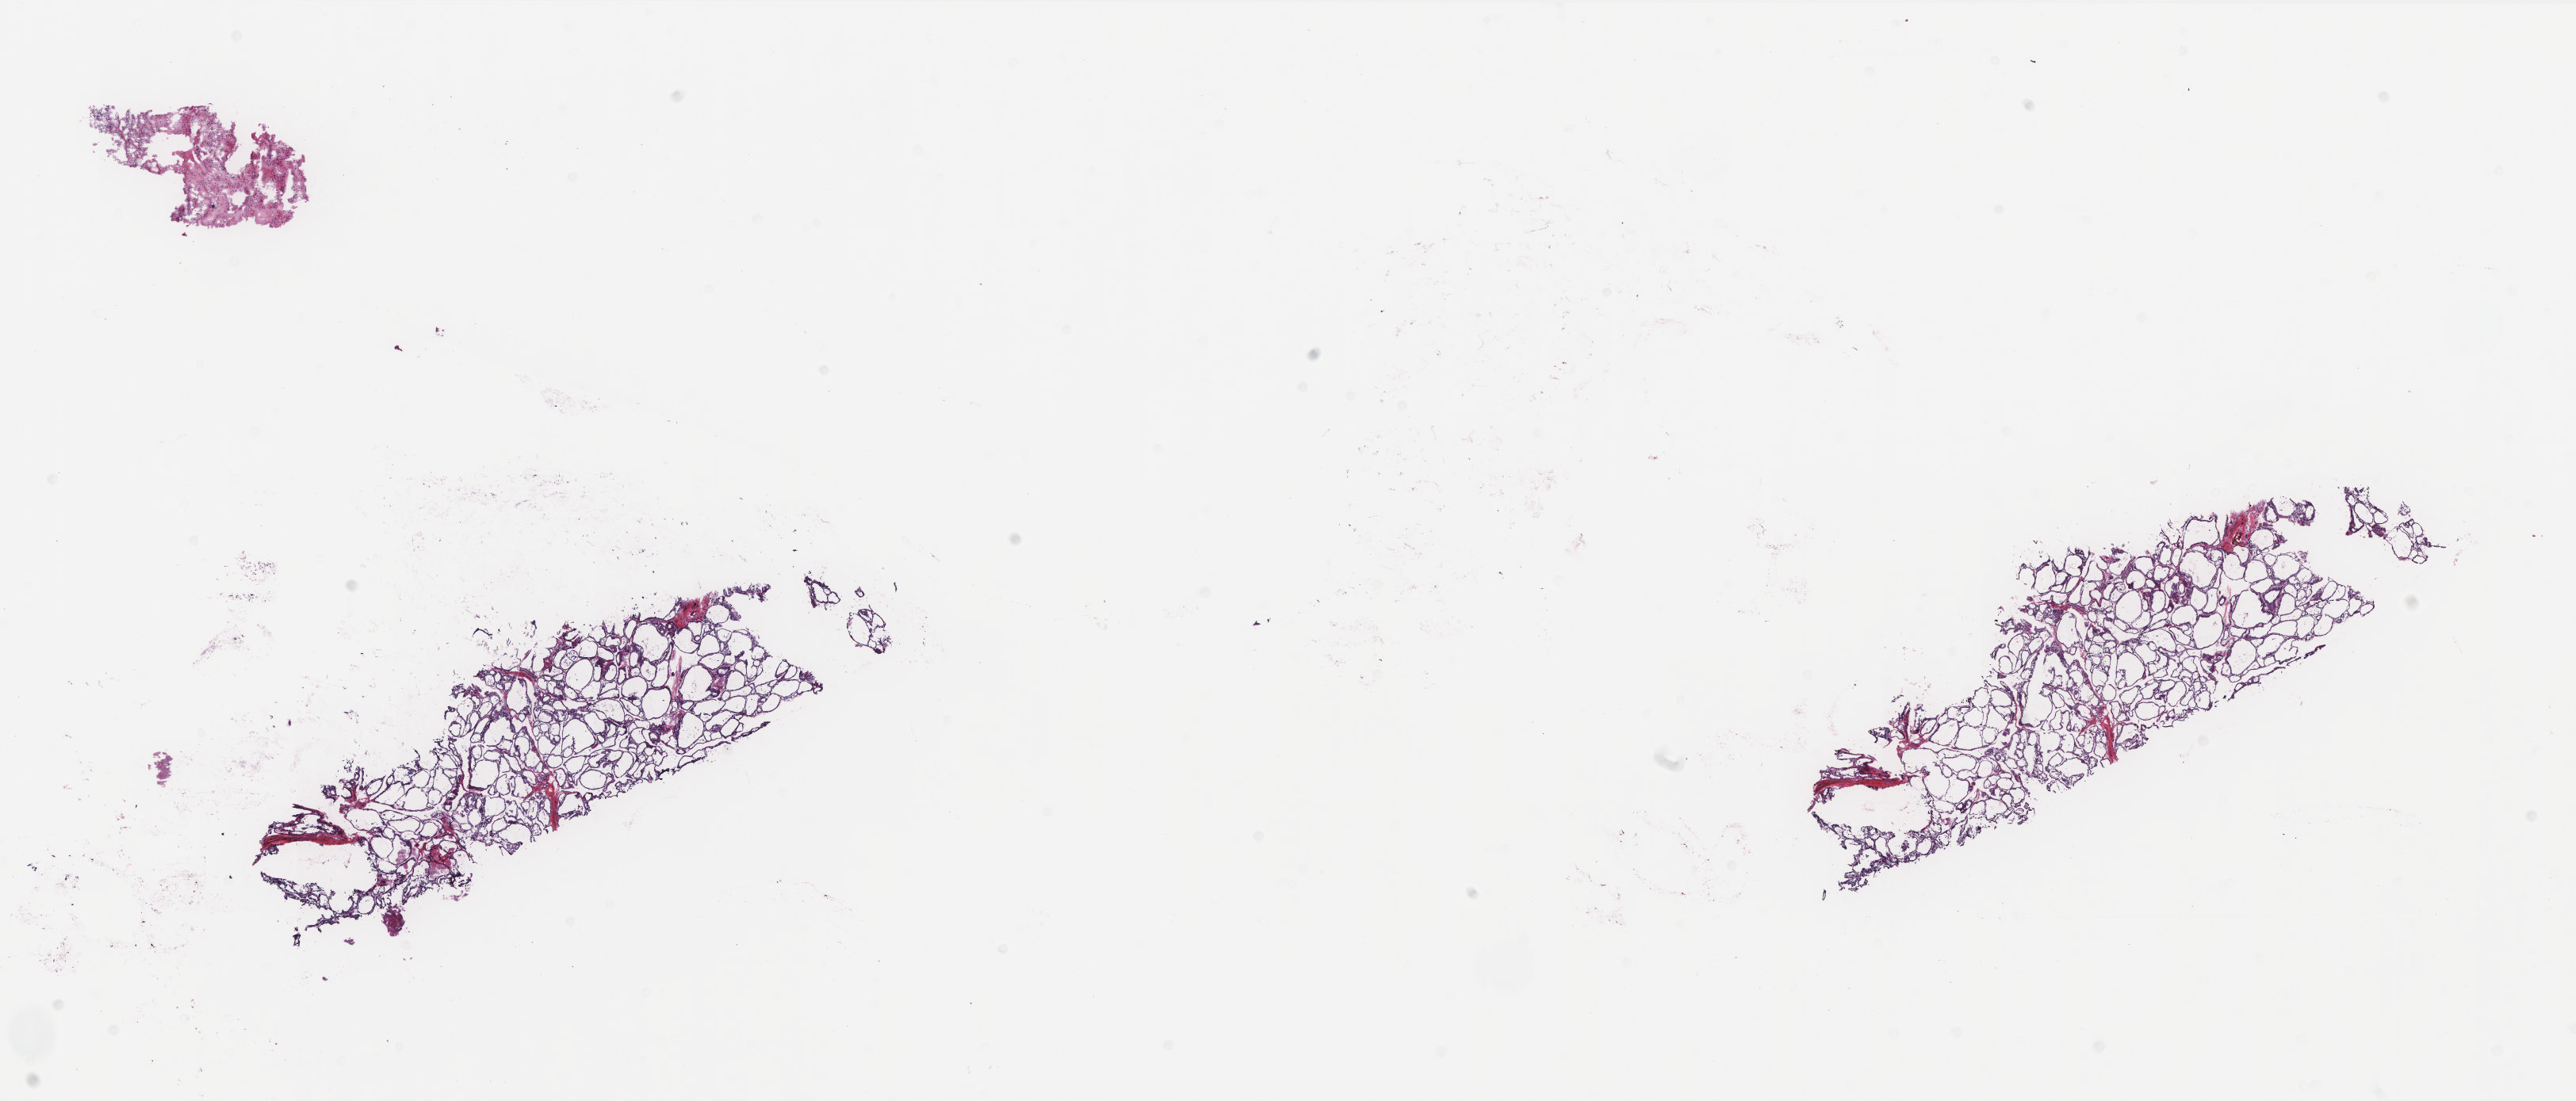
Whole-slide histology image, H&E-stained, a low-resolution overview of the entire scanned area, about 25.9 x 11.1 mm, frozen section from the top of the tissue portion, sample: solid tissue normal (non-tumour tissue), thyroid. Female, age 30 years at initial diagnosis. Composition of this section per pathologist review: tumour cells 0%, tumour nuclei 0%, normal cells 100%, stromal cells 0%, necrosis 0%. Infiltration values recorded for this section: lymphocyte infiltration 5%, monocyte infiltration 0%, neutrophil infiltration 0%.
This section: solid tissue normal sample (biorepository sample class). Patient diagnosis: Papillary adenocarcinoma, NOS (thyroid gland).